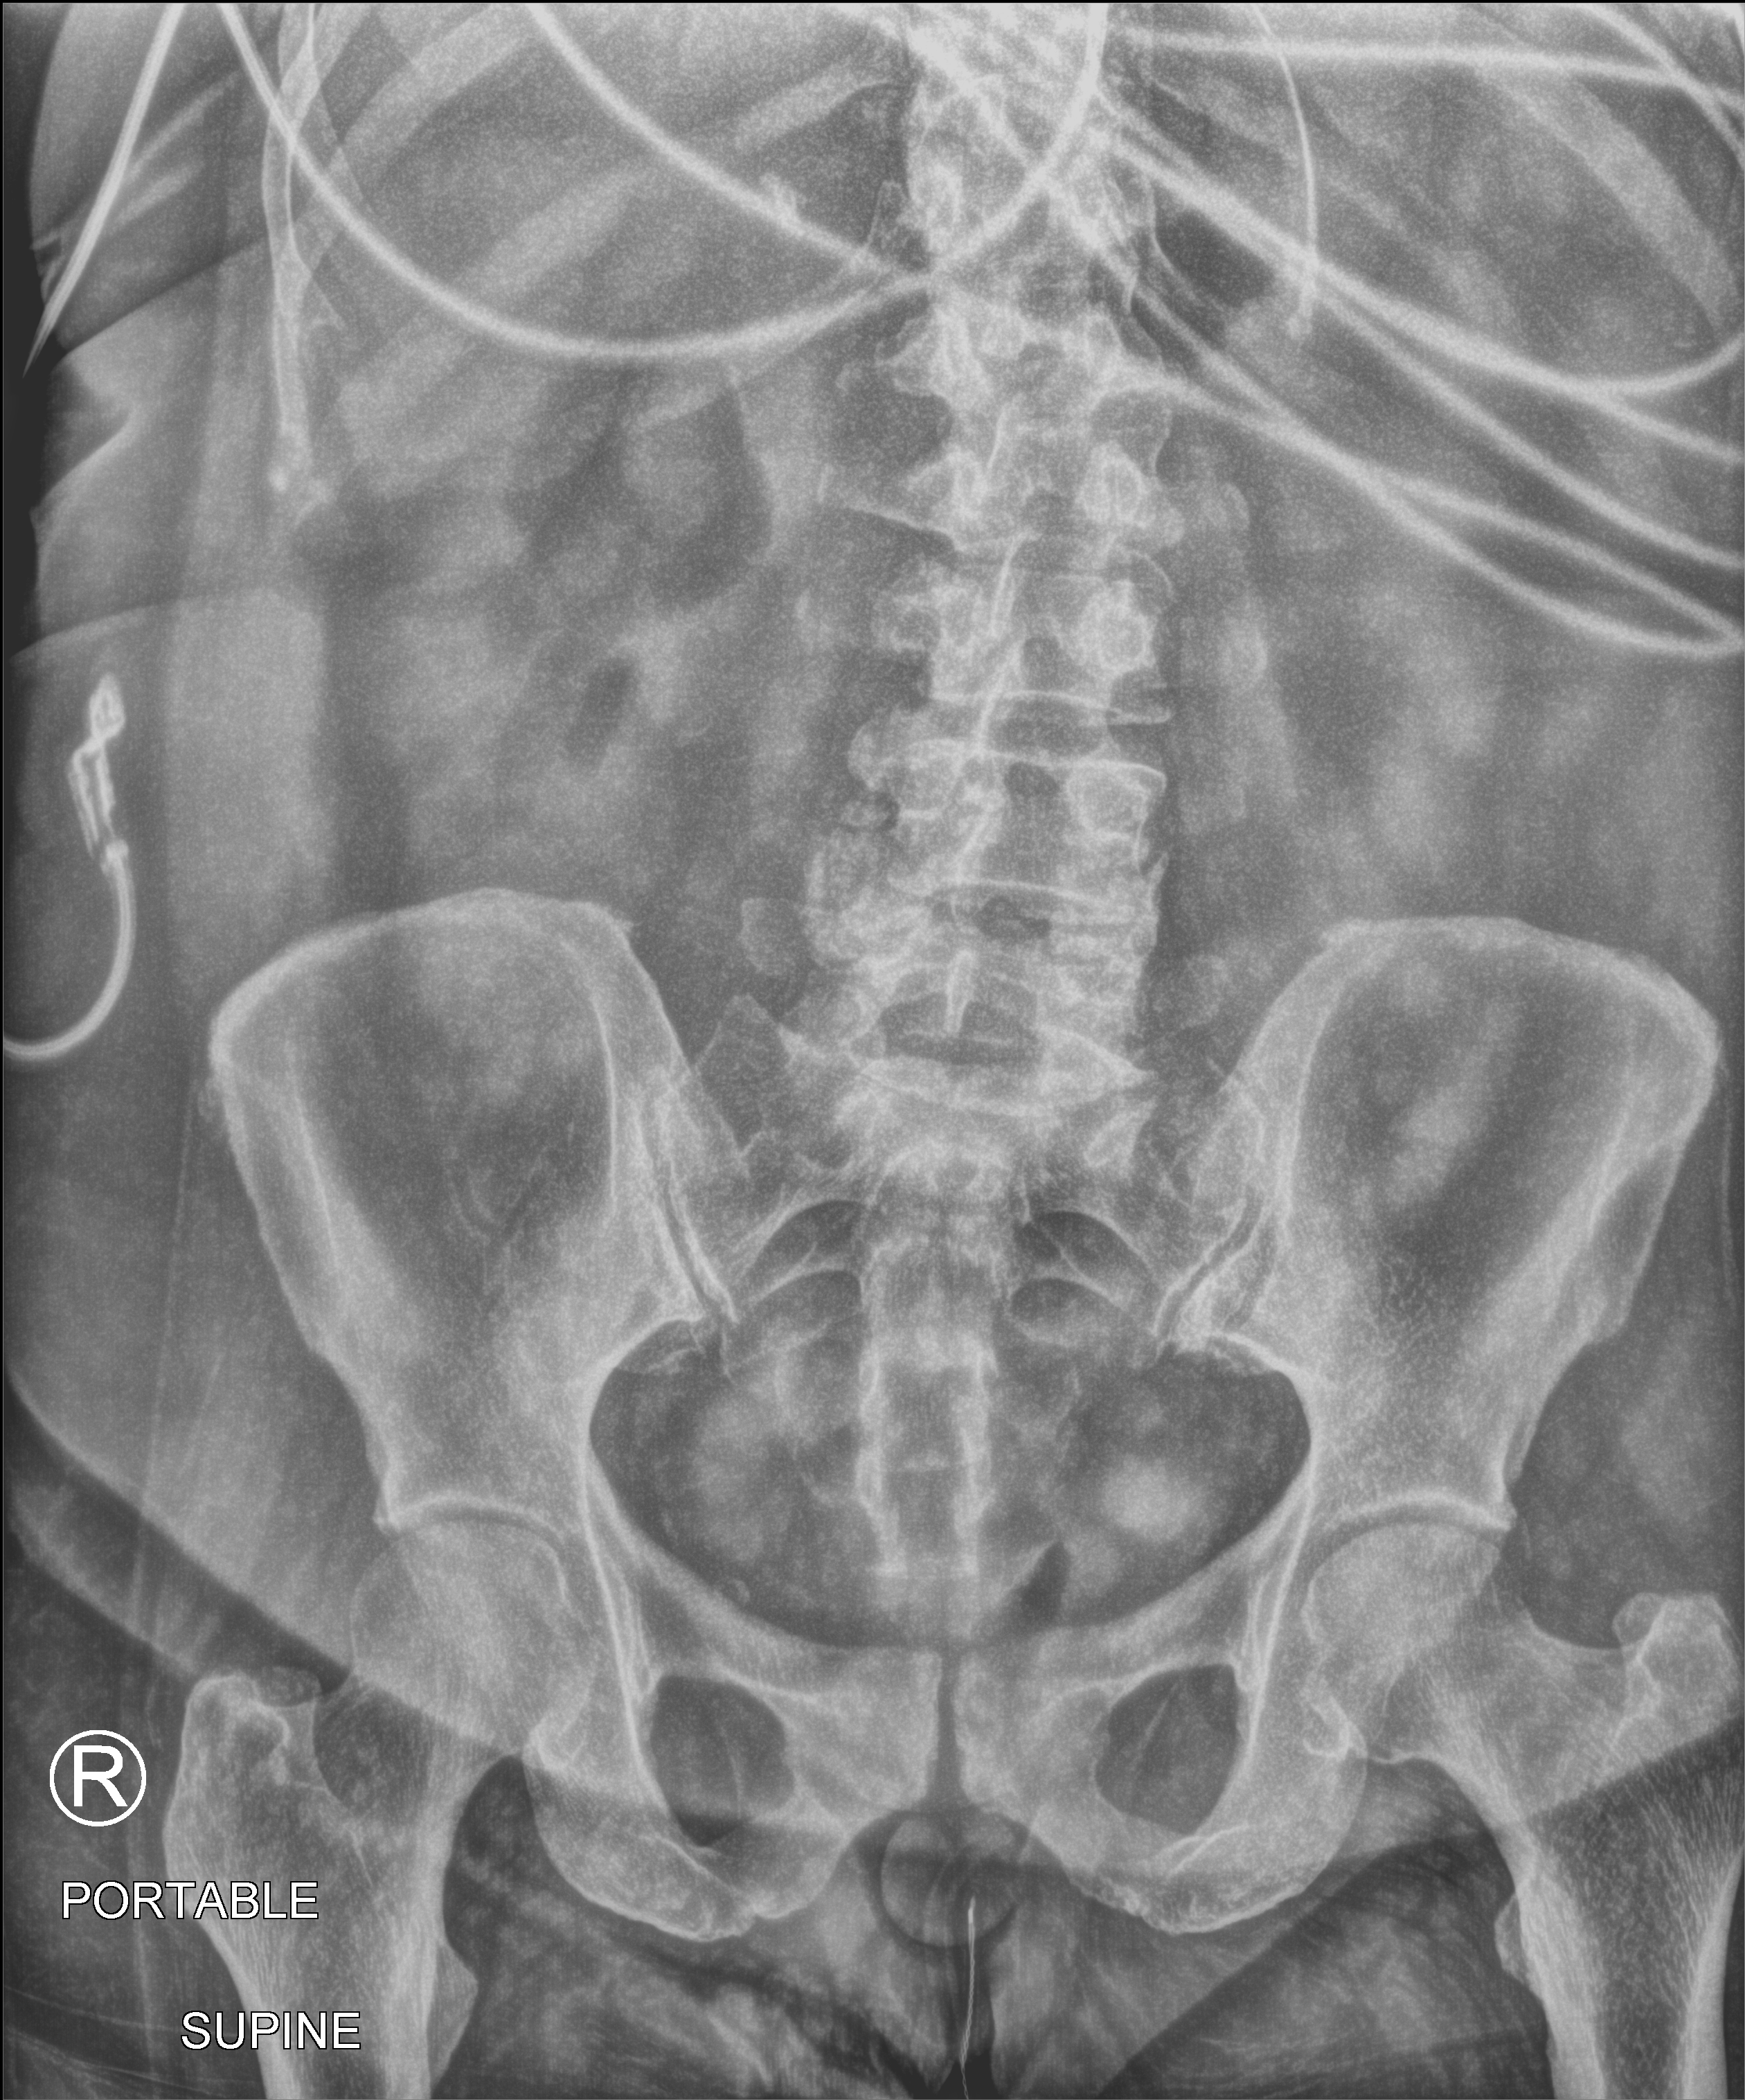
Portable abdomen radiograph; anteroposterior (AP) projection. Patient hospitalised with COVID-19; female, aged 60–74 years.
Hospital-stay facts (about this admission, not read from this image; timing relative to this image not recorded): smoking status (admission record): never; mechanically ventilated during this hospital stay: yes; length of hospital stay: 45 days.